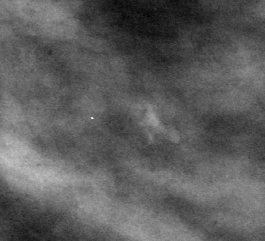
Region of interest cut from a scanned film mammogram (one marked finding); left breast; MLO view.
Calcifications, morphology dystrophic, distribution clustered; BI-RADS assessment category 3; subtlety rating 3 on a 1 (subtle) to 5 (obvious) scale; pathology (as recorded): benign.